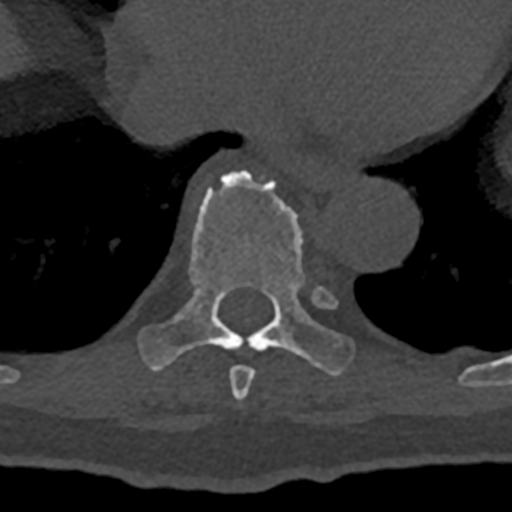
CT including the spine, one axial slice. Position 664 of 797 along the scan axis. Bone window (W 1800 / L 400 HU). 512 × 512 image matrix, field of view 160 × 160 mm. Male patient, age 74 years. Case-level facts recorded for this patient, not image findings: primary cancer: renal; vertebrae with lytic lesions (as recorded): T10, L1, L2, L3, L4, L5.
Annotated regions visible in this slice (semi-automatic segmentation, software-assisted and operator-edited):
- T8 vertebra: bounding box <229,366,255,400> (left, top, right, bottom; pixels)
- T9 vertebra: <140,171,353,376>